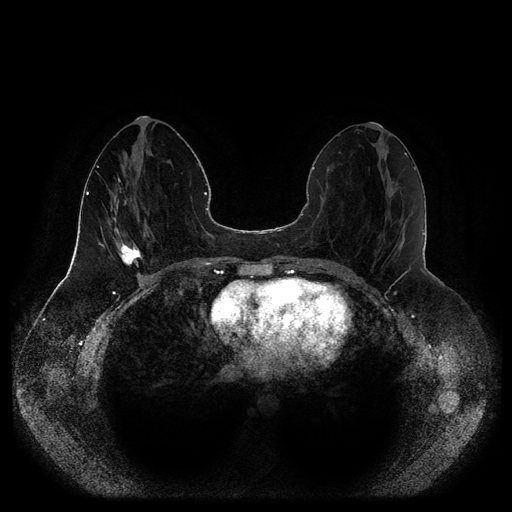
Breast MRI (dynamic contrast-enhanced, multi-phase), one axial slice; slice 42 of 116 in the series (ordered by position); dynamic contrast-enhanced series, time point 2 of 5 at this slice position (early post-contrast); 1.5 T; TE 2.5 ms, TR 5.2 ms; 512 × 512 image matrix. Patient: female, 44 years.
Outlined on this slice (semi-automatic segmentation, software-assisted and operator-edited):
- breast lesion (labelled 'tumour' in the annotation; benign lesions carry a separate 'benign' label): bounding box [x1, y1, x2, y2] px = [117, 241, 141, 268]
- breast lesion (labelled 'tumour' in the annotation; benign lesions carry a separate 'benign' label): [95, 170, 111, 193]